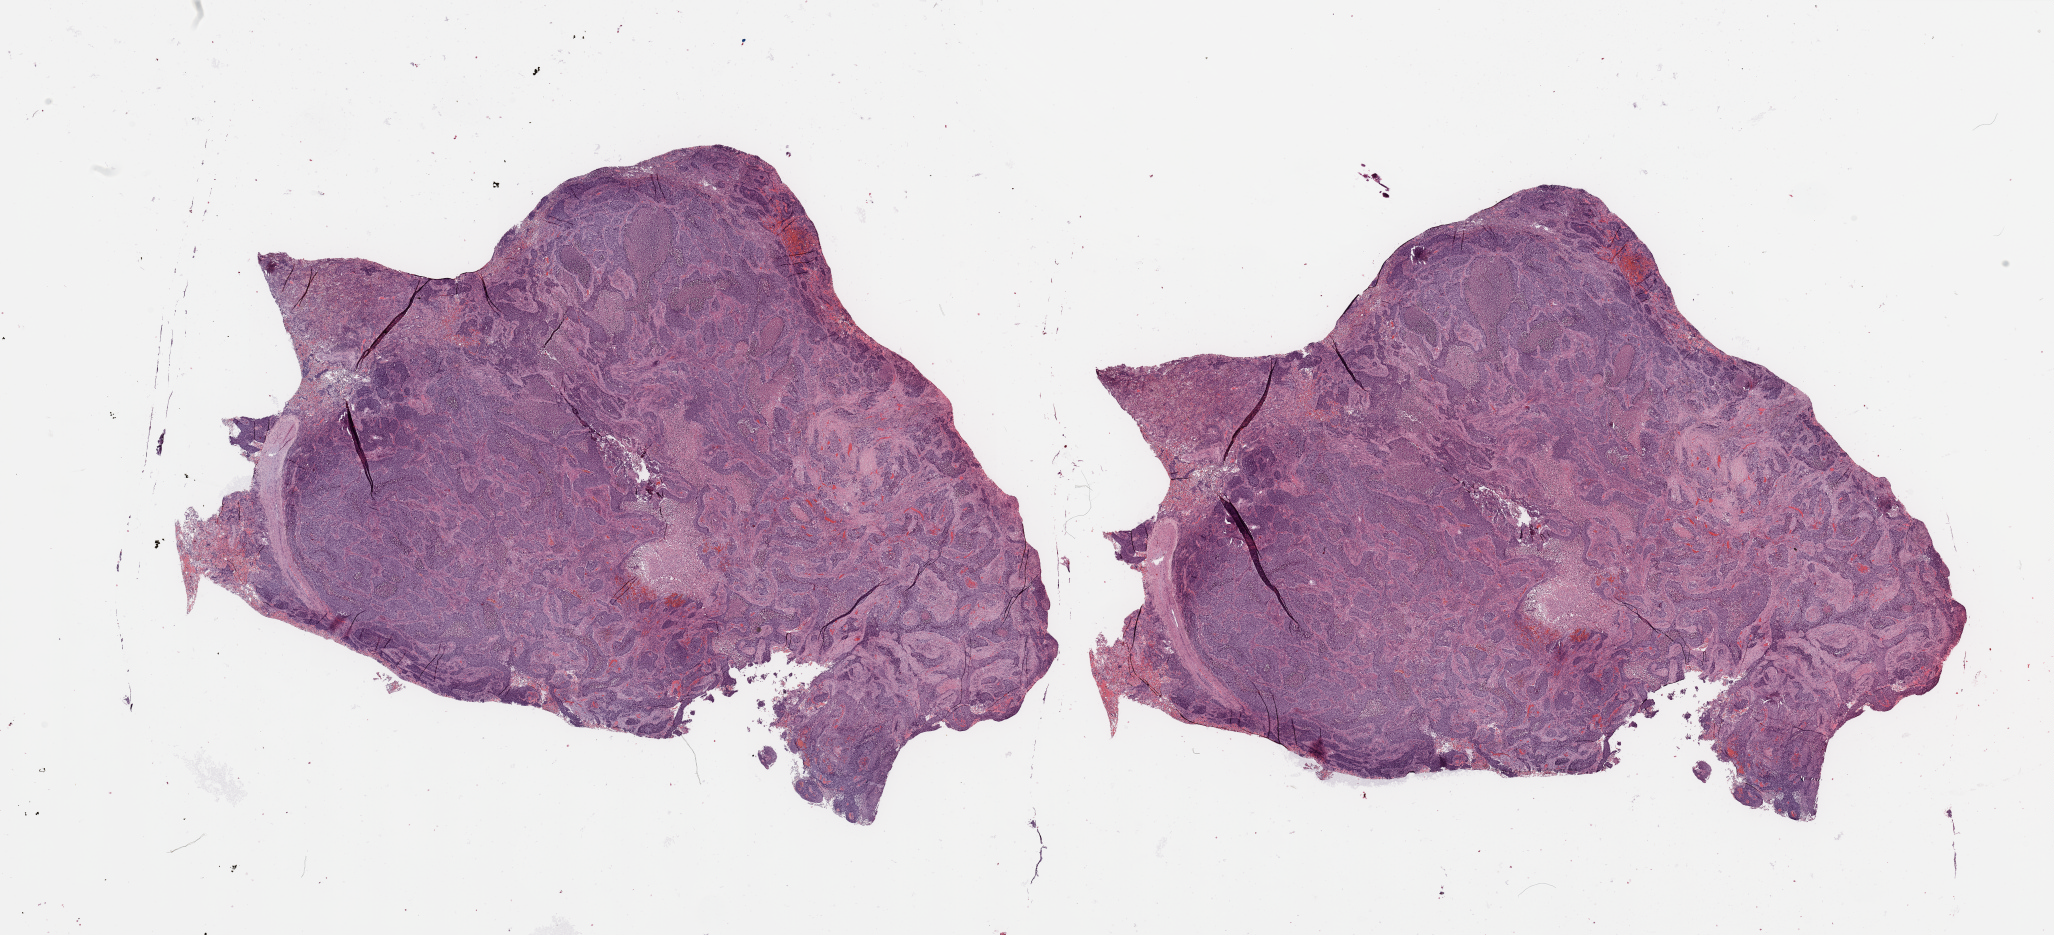
Whole-slide histology image, H&E — a low-resolution overview of the entire scanned area, about 32.5 x 14.8 mm; tumour tissue sample, lung. Patient: male, age 73 years. Histologic grade: G3 (poorly differentiated).
* primary tumour site (as recorded): left upper lobe
* histologic diagnosis: Squamous cell carcinoma, NOS
* AJCC pathologic stage: IIB